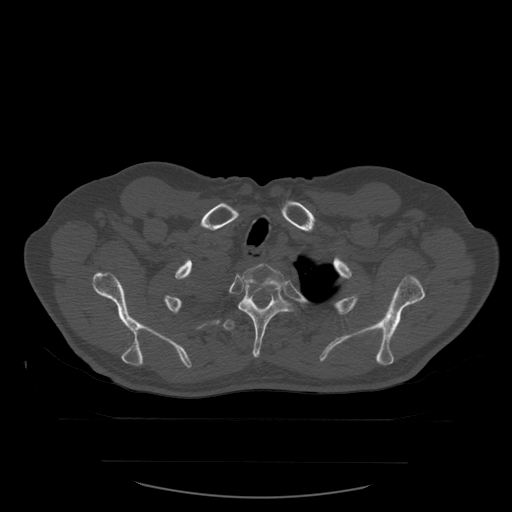
CT including the spine, one axial slice; position 460 of 590 along the scan axis; bone window (W 1800 / L 400 HU); 1.25 mm slice thickness; 512 × 512 image matrix. Patient age 71 years. From the clinical record (not read from this slice): primary cancer: lung; vertebrae with lytic lesions (as recorded): T1, T2, L5, S1.
Annotated regions visible in this slice (semi-automatic segmentation, software-assisted and operator-edited):
- T2 vertebra: box from (x=243, y=264) to (x=286, y=290) px
- T3 vertebra: (x=238, y=286)–(x=300, y=358)
- T4 vertebra: (x=223, y=303)–(x=255, y=332)